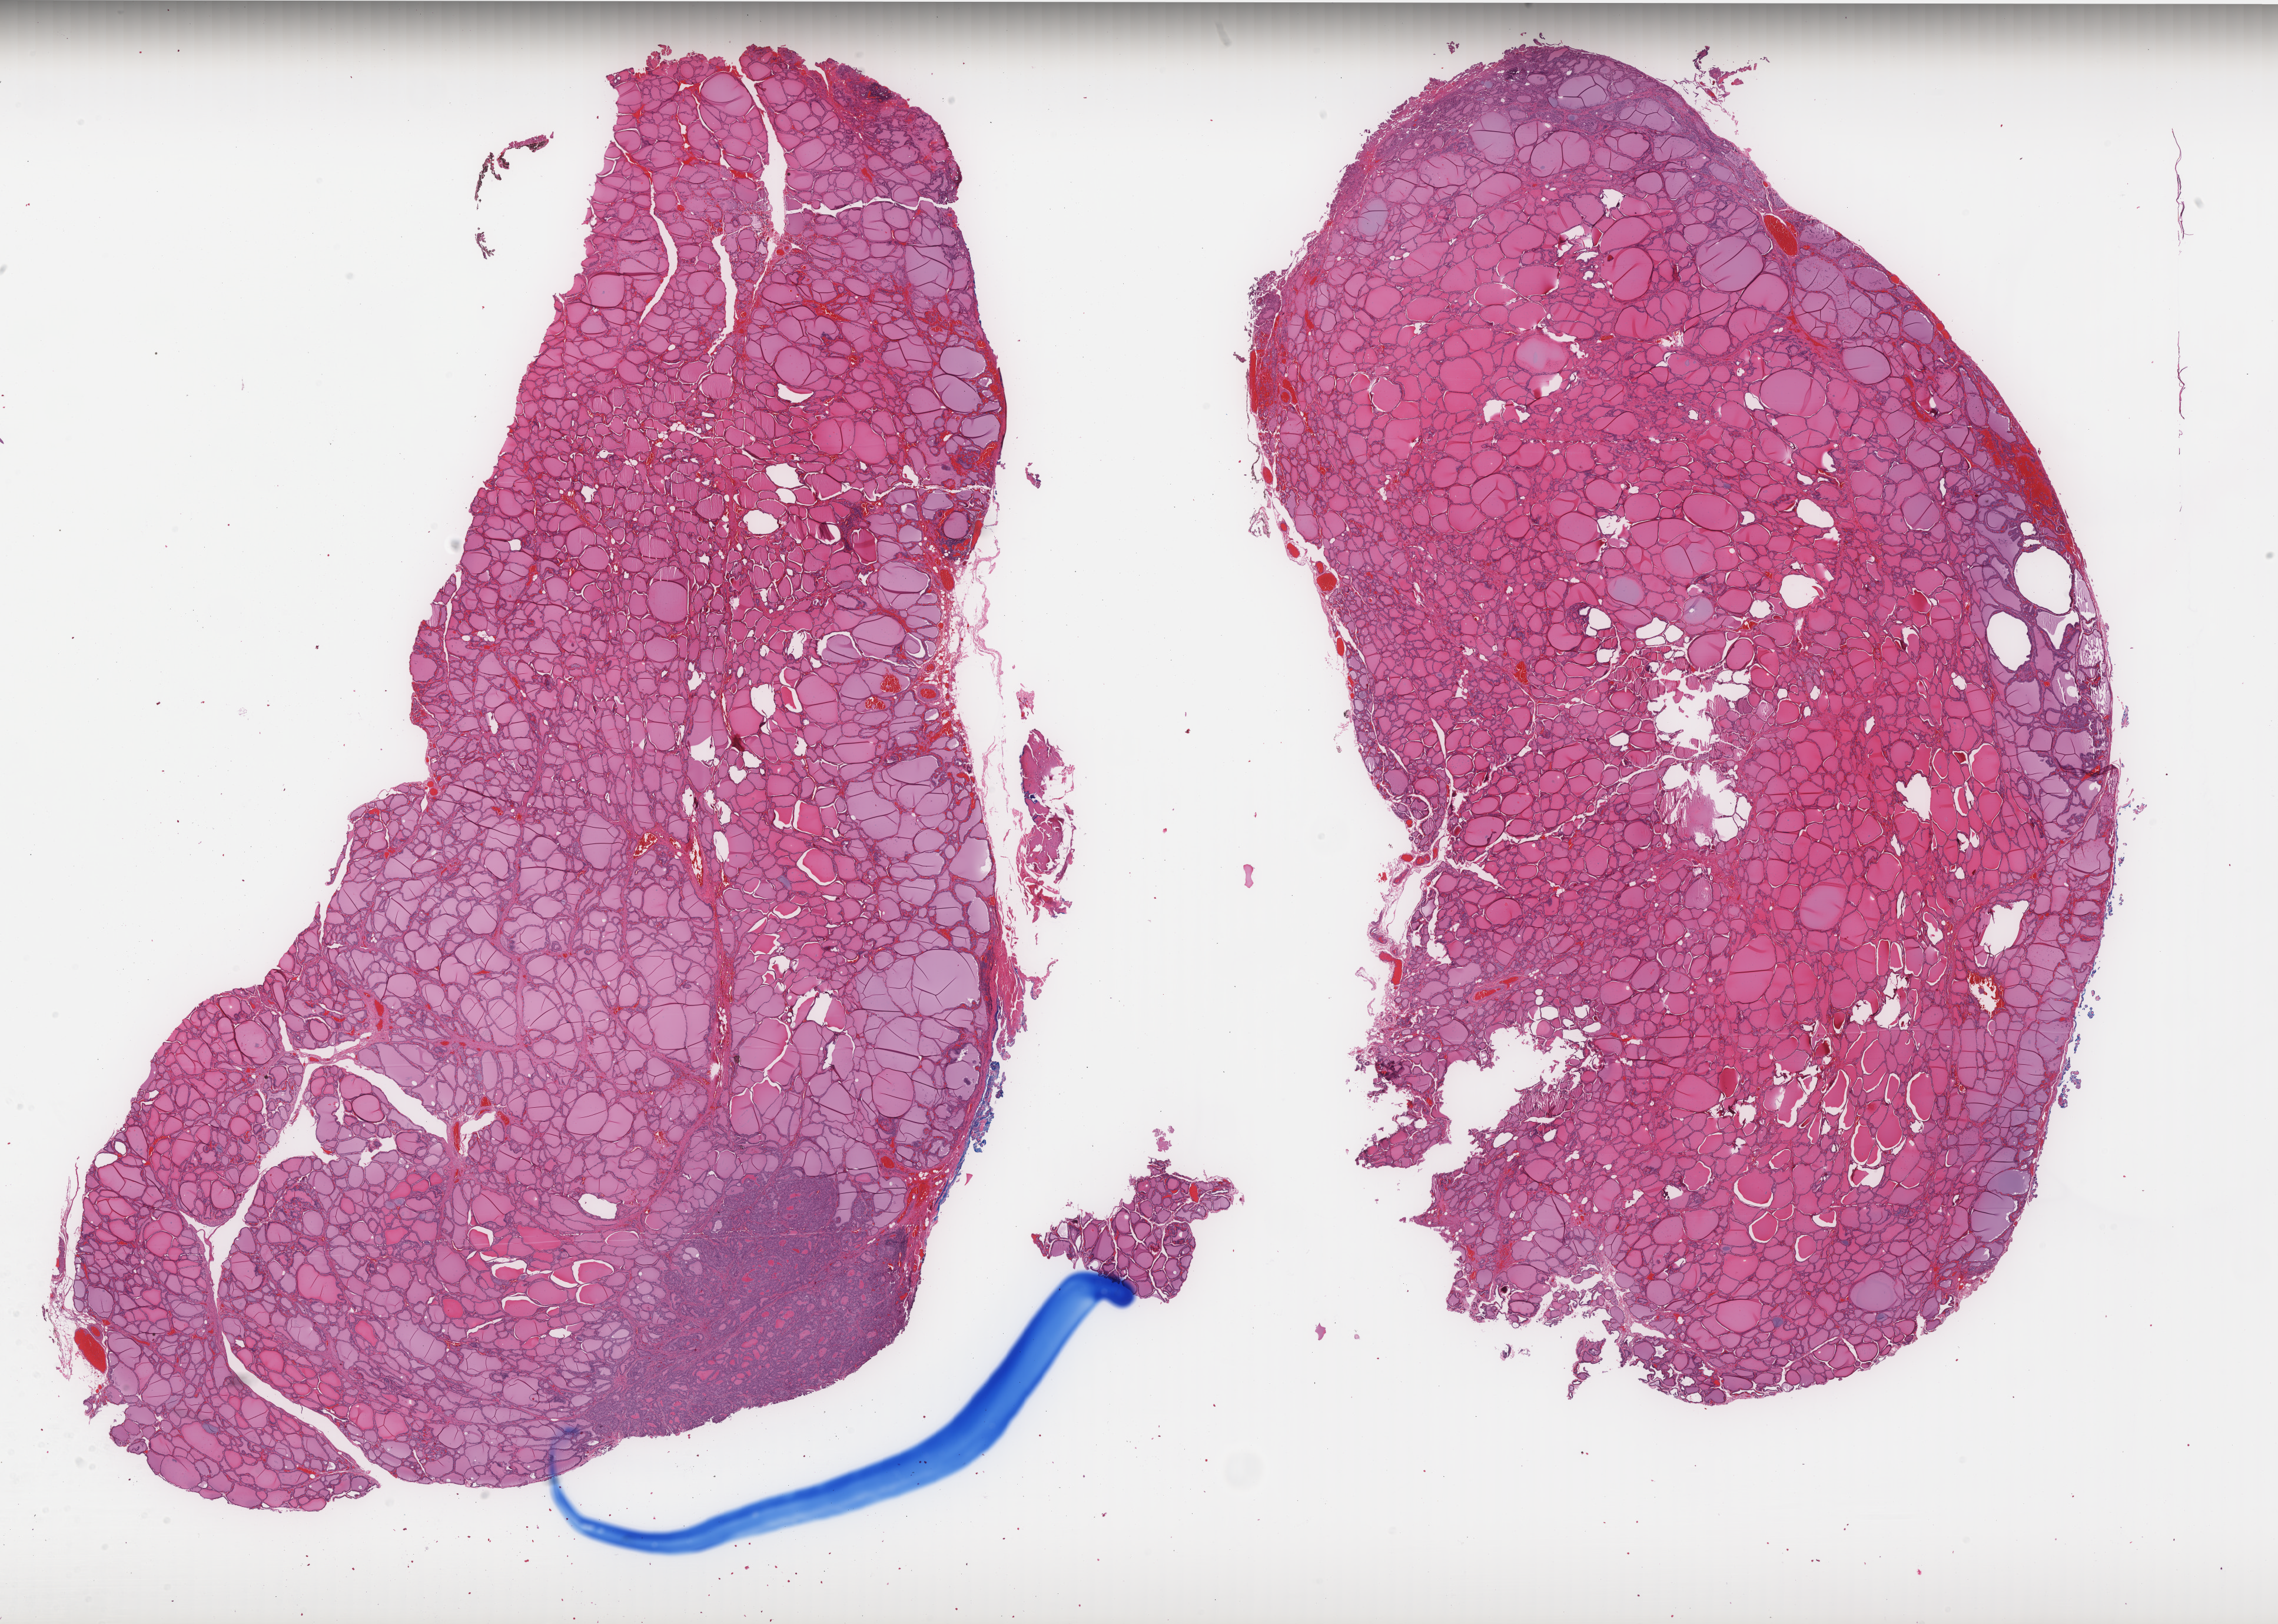
Hematoxylin and eosin (H&E) stained whole-slide image, whole scanned area (about 31.0 x 22.1 mm, from a 40x scan) shown as a low-resolution overview, FFPE section, thyroid, primary tumour sample. Male patient; age at initial diagnosis 42 years.
Diagnosis: Papillary carcinoma, follicular variant (thyroid gland). AJCC pathologic stage: I (7th edition). Lymph nodes positive (case pathology): 0 of 2 examined. Laterality: bilateral.